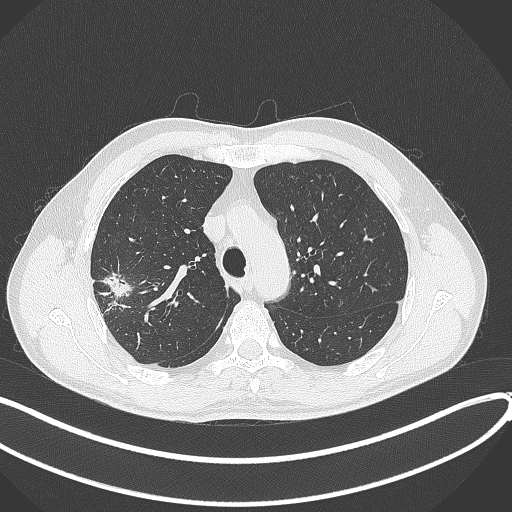
Chest CT, one axial slice; slice 309 of 381 in the series (ordered by position); reconstruction kernel B70f; 120 kVp; lung window (W 1500 / L -600 HU); 1 mm slice thickness; 512 × 512 image matrix. Patient: male, 62 years. From the clinical record (not read from this slice): clinical TNM (as recorded): T1c N0 M0.
Outlined on this slice (bounding box drawn by a radiologist):
- lung tumour (recorded histology: adenocarcinoma): bounding box [x1, y1, x2, y2] px = [101, 267, 133, 302]